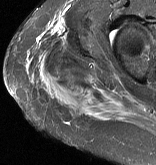
MRI of an extremity soft-tissue mass, one axial slice; position 44 of 57 along the scan axis; STIR; MR volume resampled by the dataset authors to the PET/CT grid (not the native acquisition matrix); 3.27 mm slice thickness; 156 × 165 image matrix. Female patient. From the clinical record (not read from this slice): histological type: epithelioid sarcoma with vascular differentiation; site of the primary tumour: right buttock.
Structures marked on this image (expert contour drawn on MRI and transferred to this co-registered scan by the dataset authors):
- gross tumour volume (mass): bounding box [x1, y1, x2, y2] px = [44, 71, 82, 79]